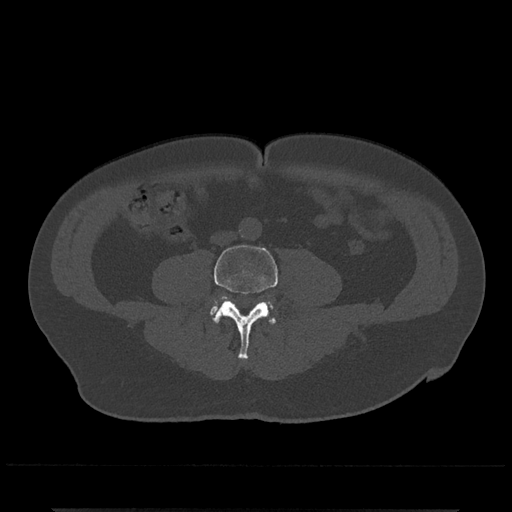
CT including the spine, one axial slice; slice 144 of 797 in the series (ordered by position); 120 kVp; bone window (W 1800 / L 400 HU); 0.5 mm slice thickness; 512 × 512 image matrix, field of view 393 × 393 mm. Male patient, age 67 years. Case-level facts recorded for this patient, not image findings: primary cancer: prostate.
Annotated regions visible in this slice (semi-automatic segmentation, software-assisted and operator-edited):
- L4 vertebra: bounding box (x1, y1, x2, y2) in pixels: (214, 244, 278, 359)
- L5 vertebra: (210, 303, 274, 315)